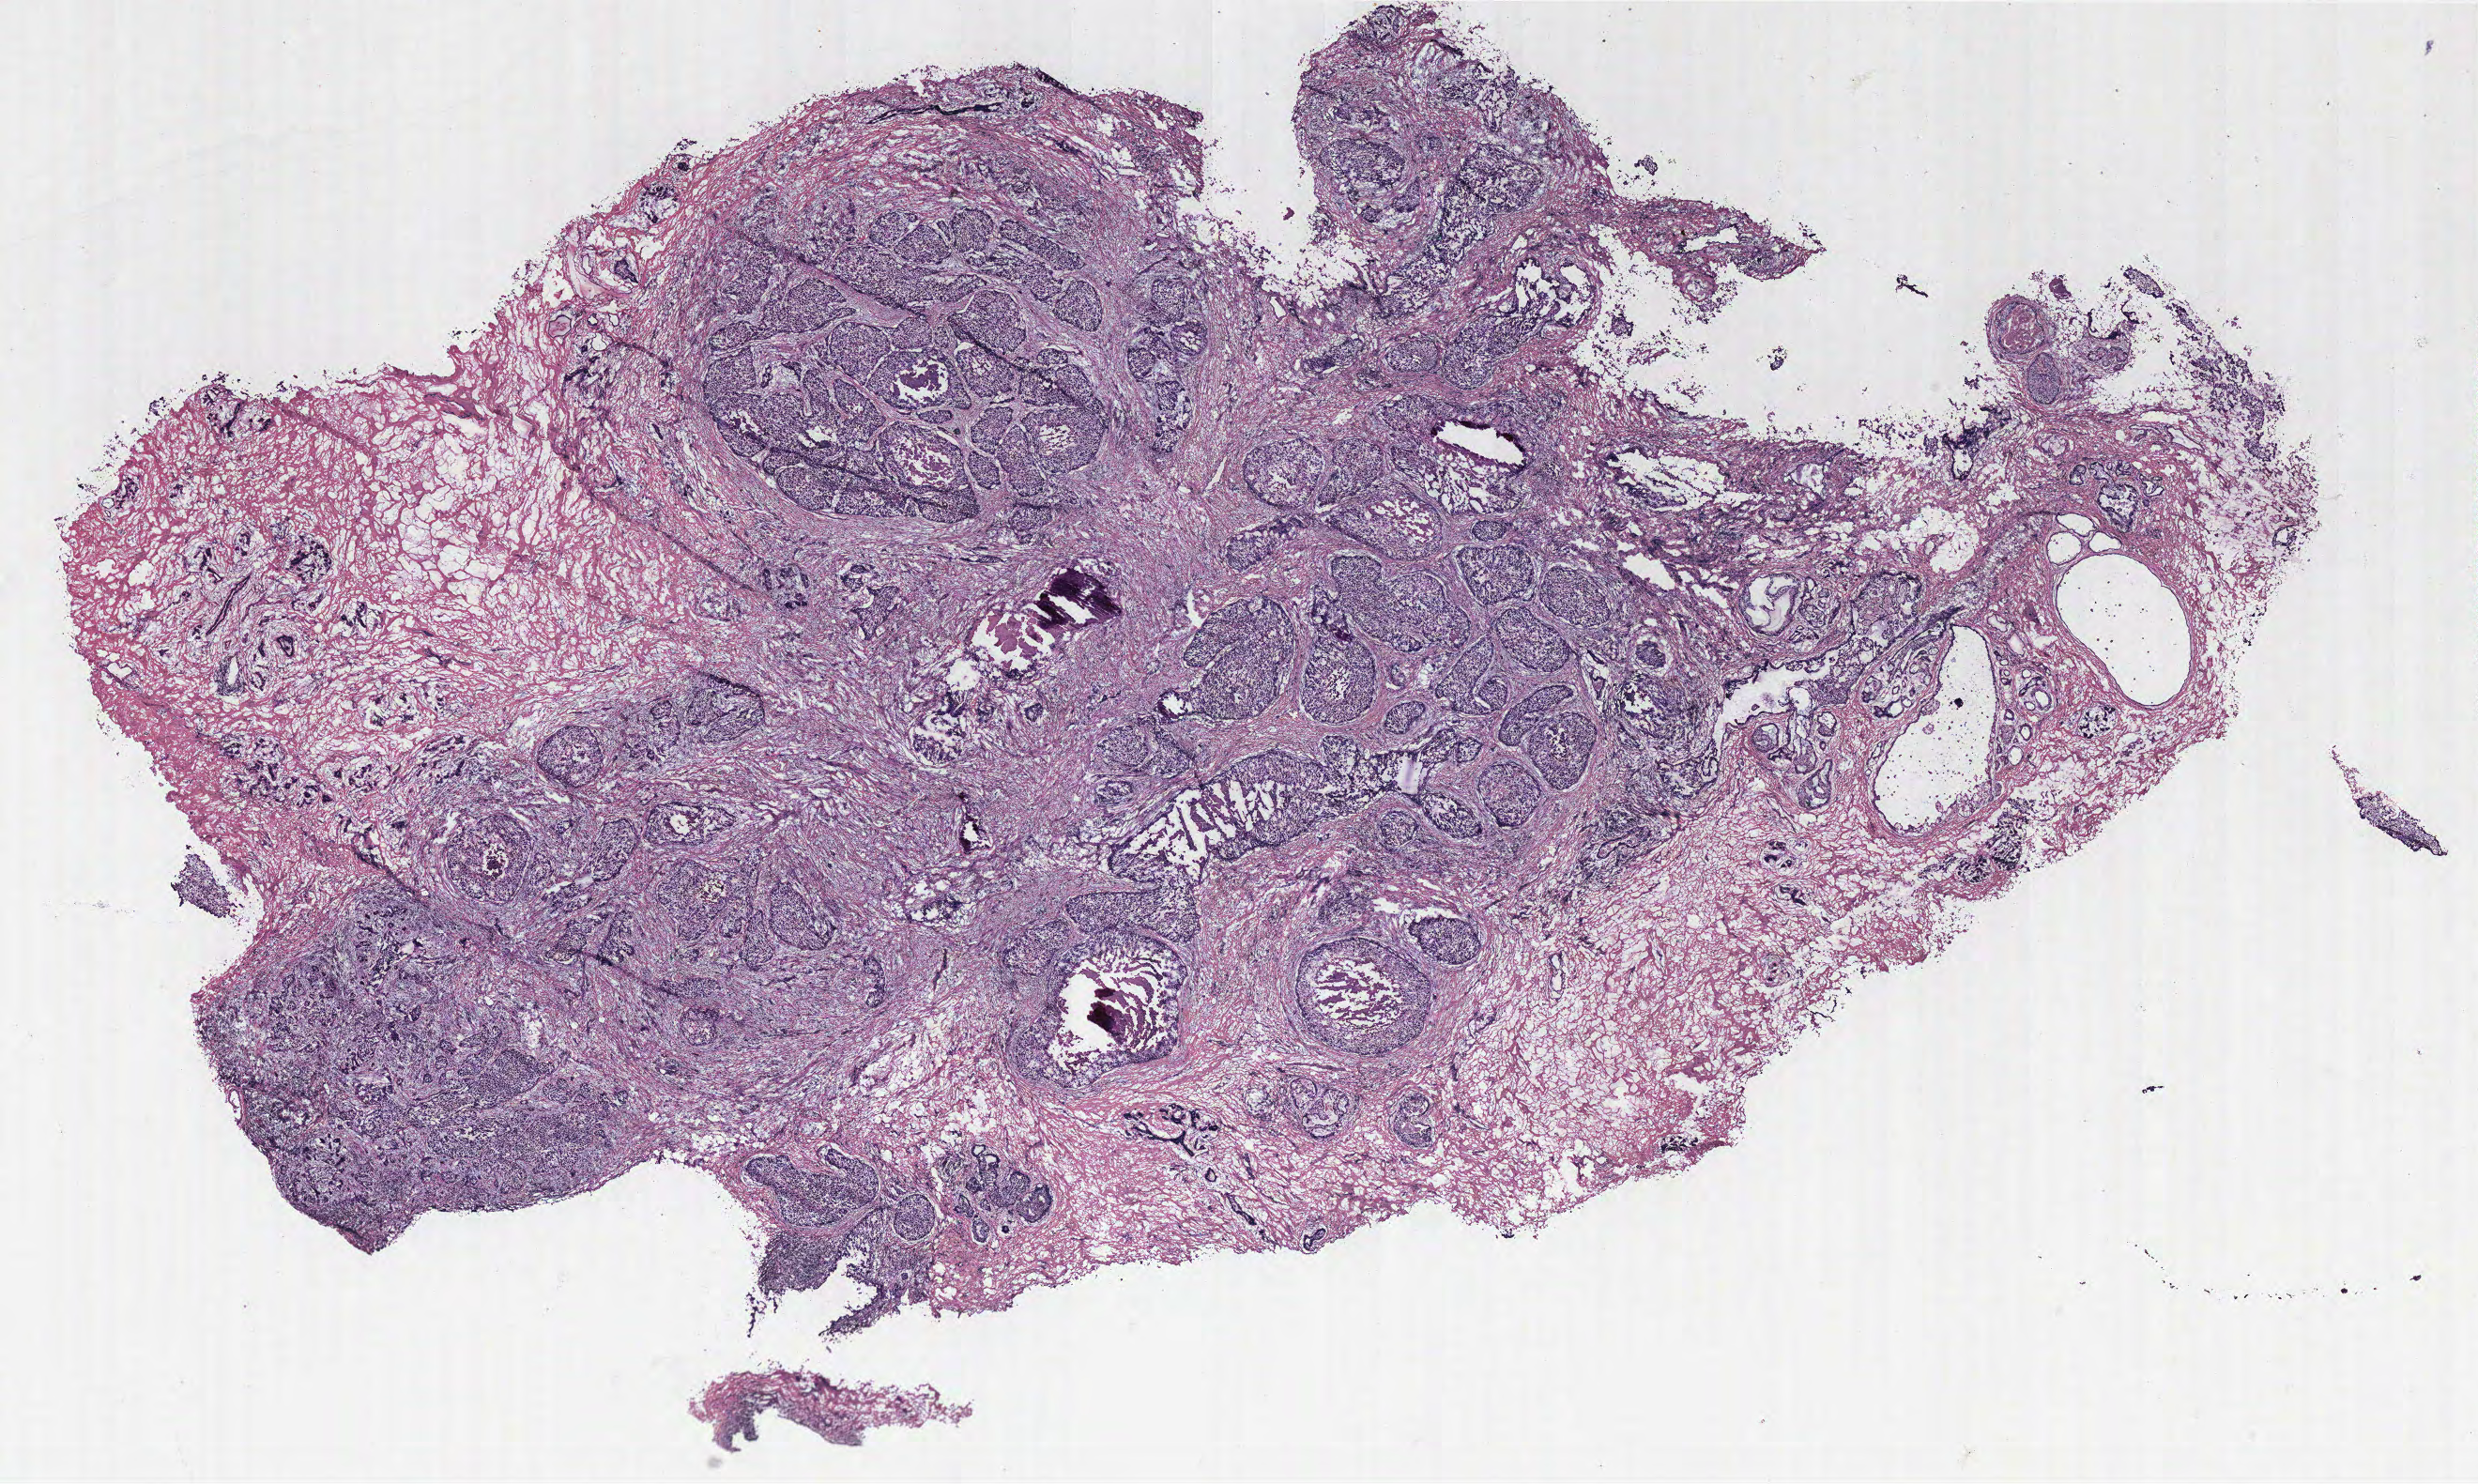
Whole-slide histology image, H&E-stained — a low-resolution overview of the entire scanned area, about 21.1 x 12.7 mm (acquisition: 40x scan). Tumour tissue sample, breast. 45-year-old female patient.
Diagnosis: Infiltrating duct carcinoma, NOS. AJCC pathologic stage: IIA.